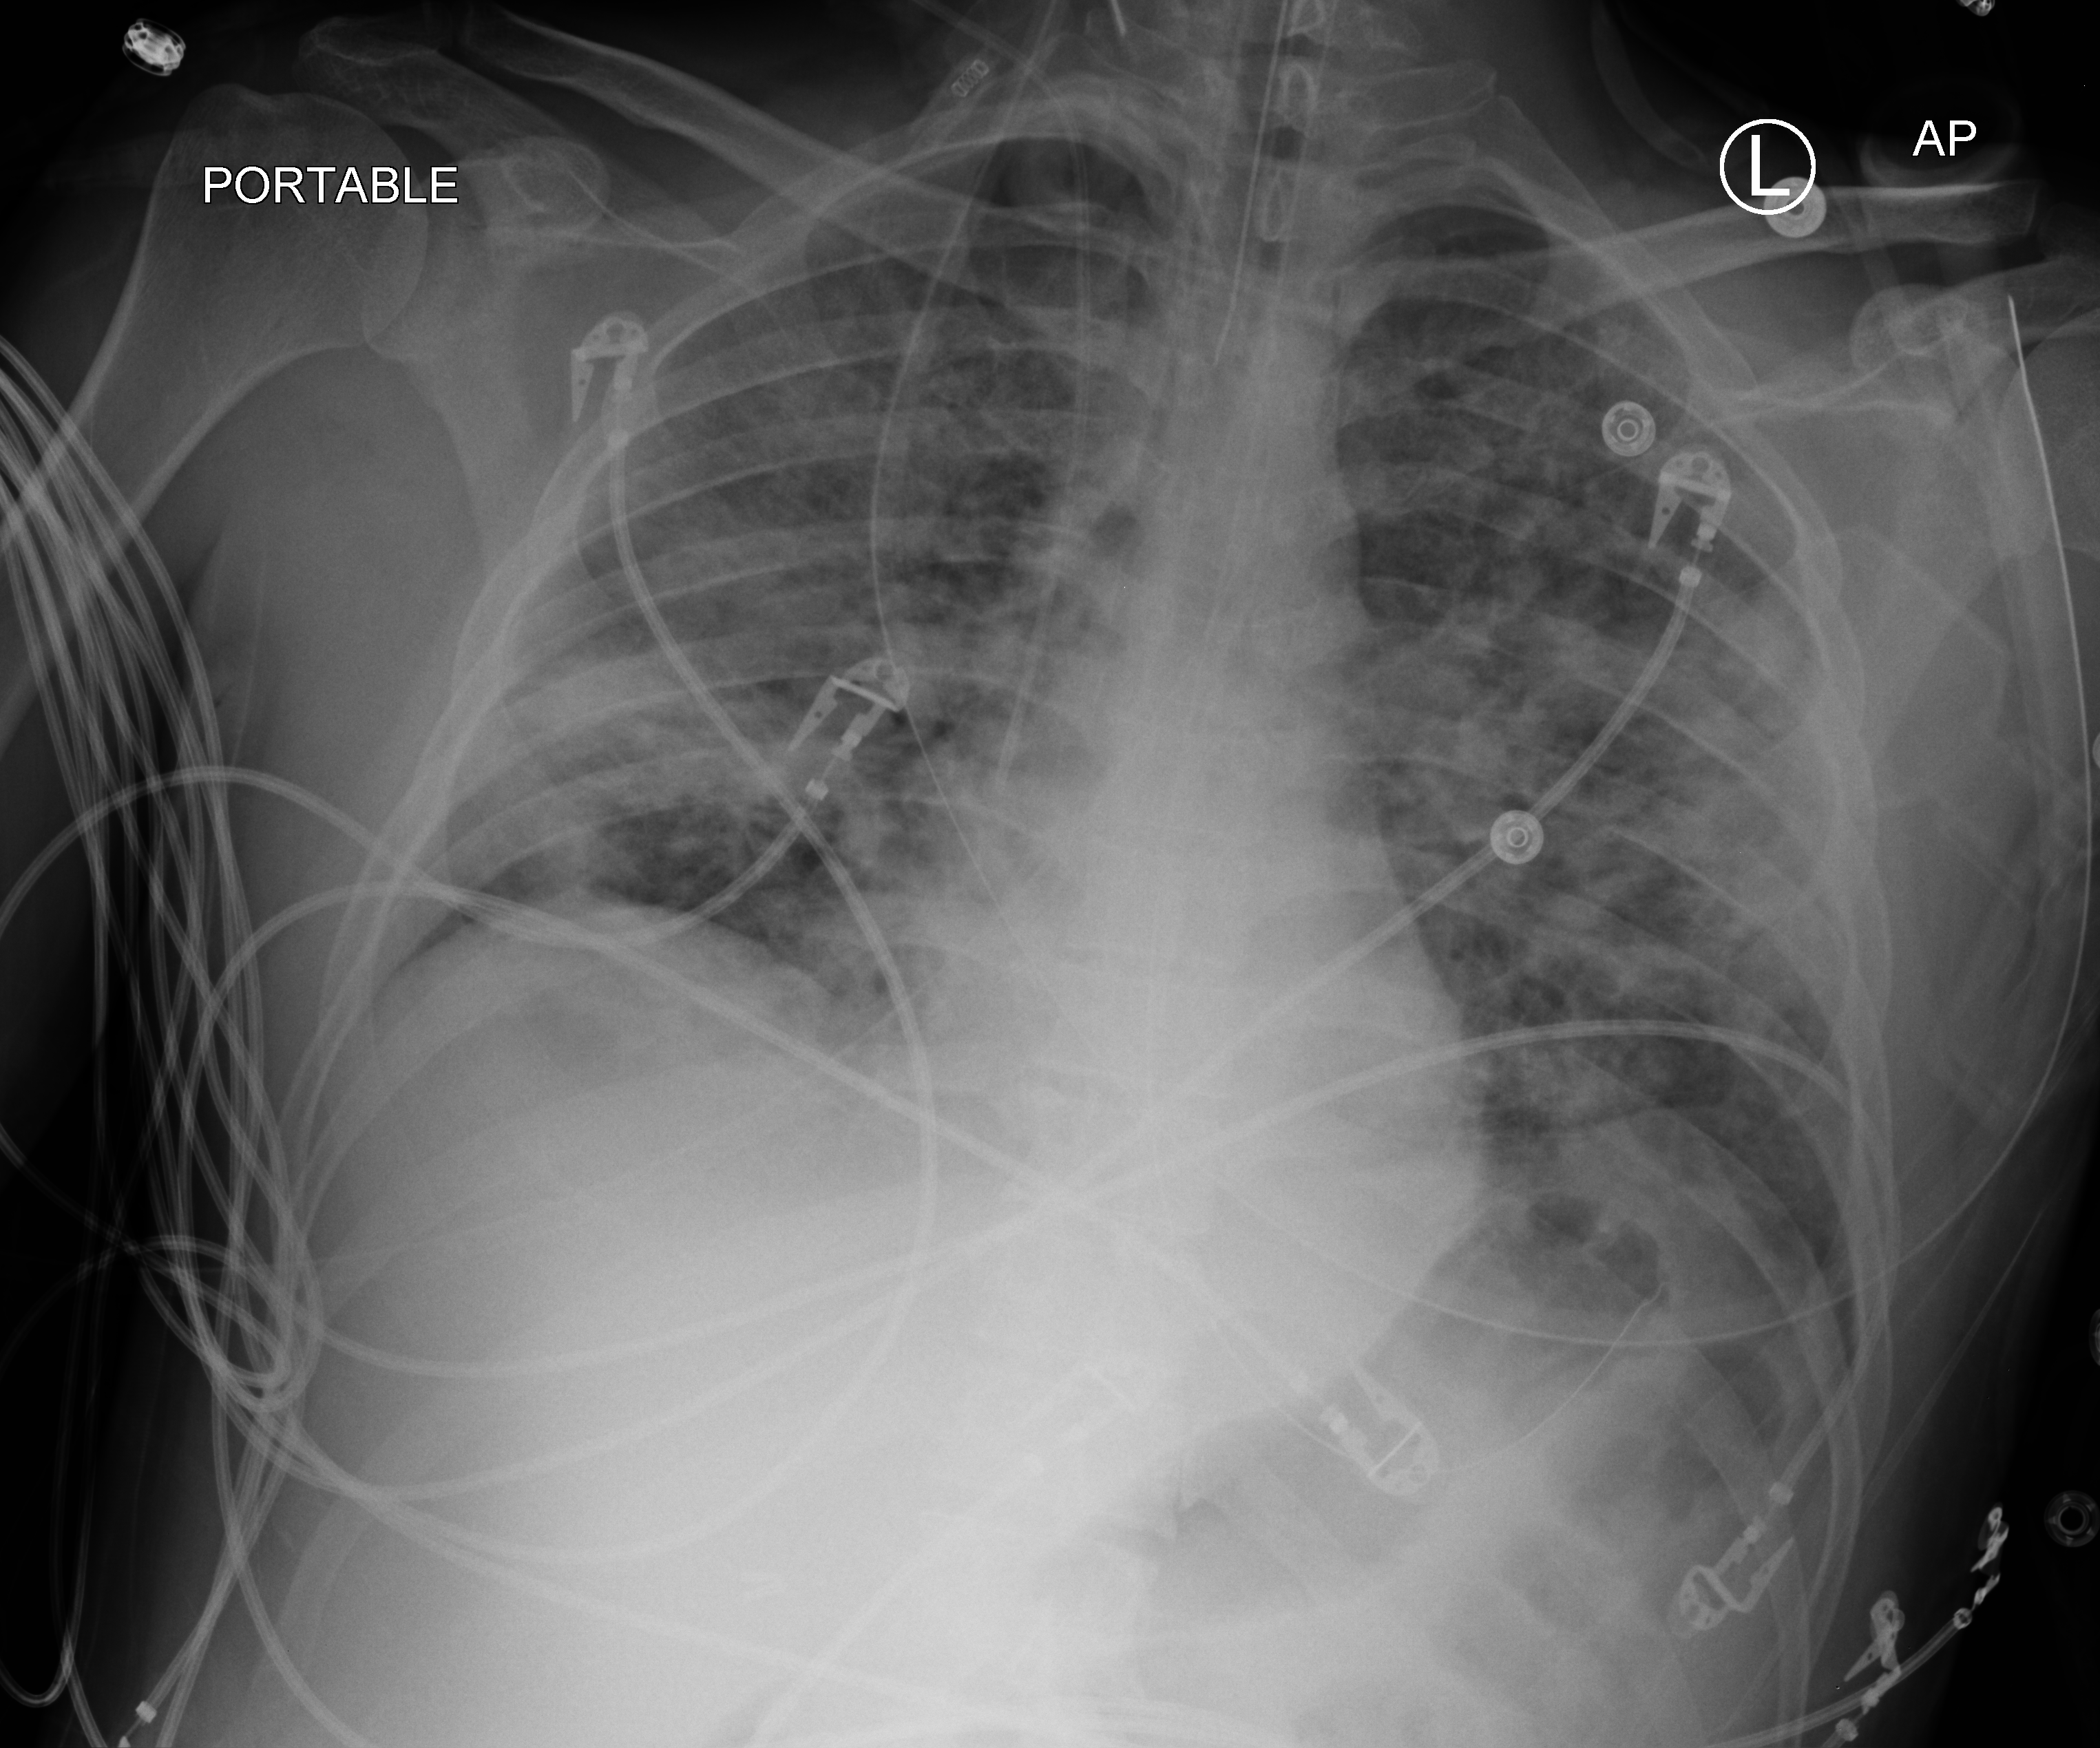
Chest X-ray (portable). Patient hospitalised with COVID-19; male, aged 18–59 years.
From the hospital-stay record, not from the radiograph (when in the stay this image was taken is not recorded): chronic kidney disease (admission record): no; admitted to intensive care during this hospital stay: yes.